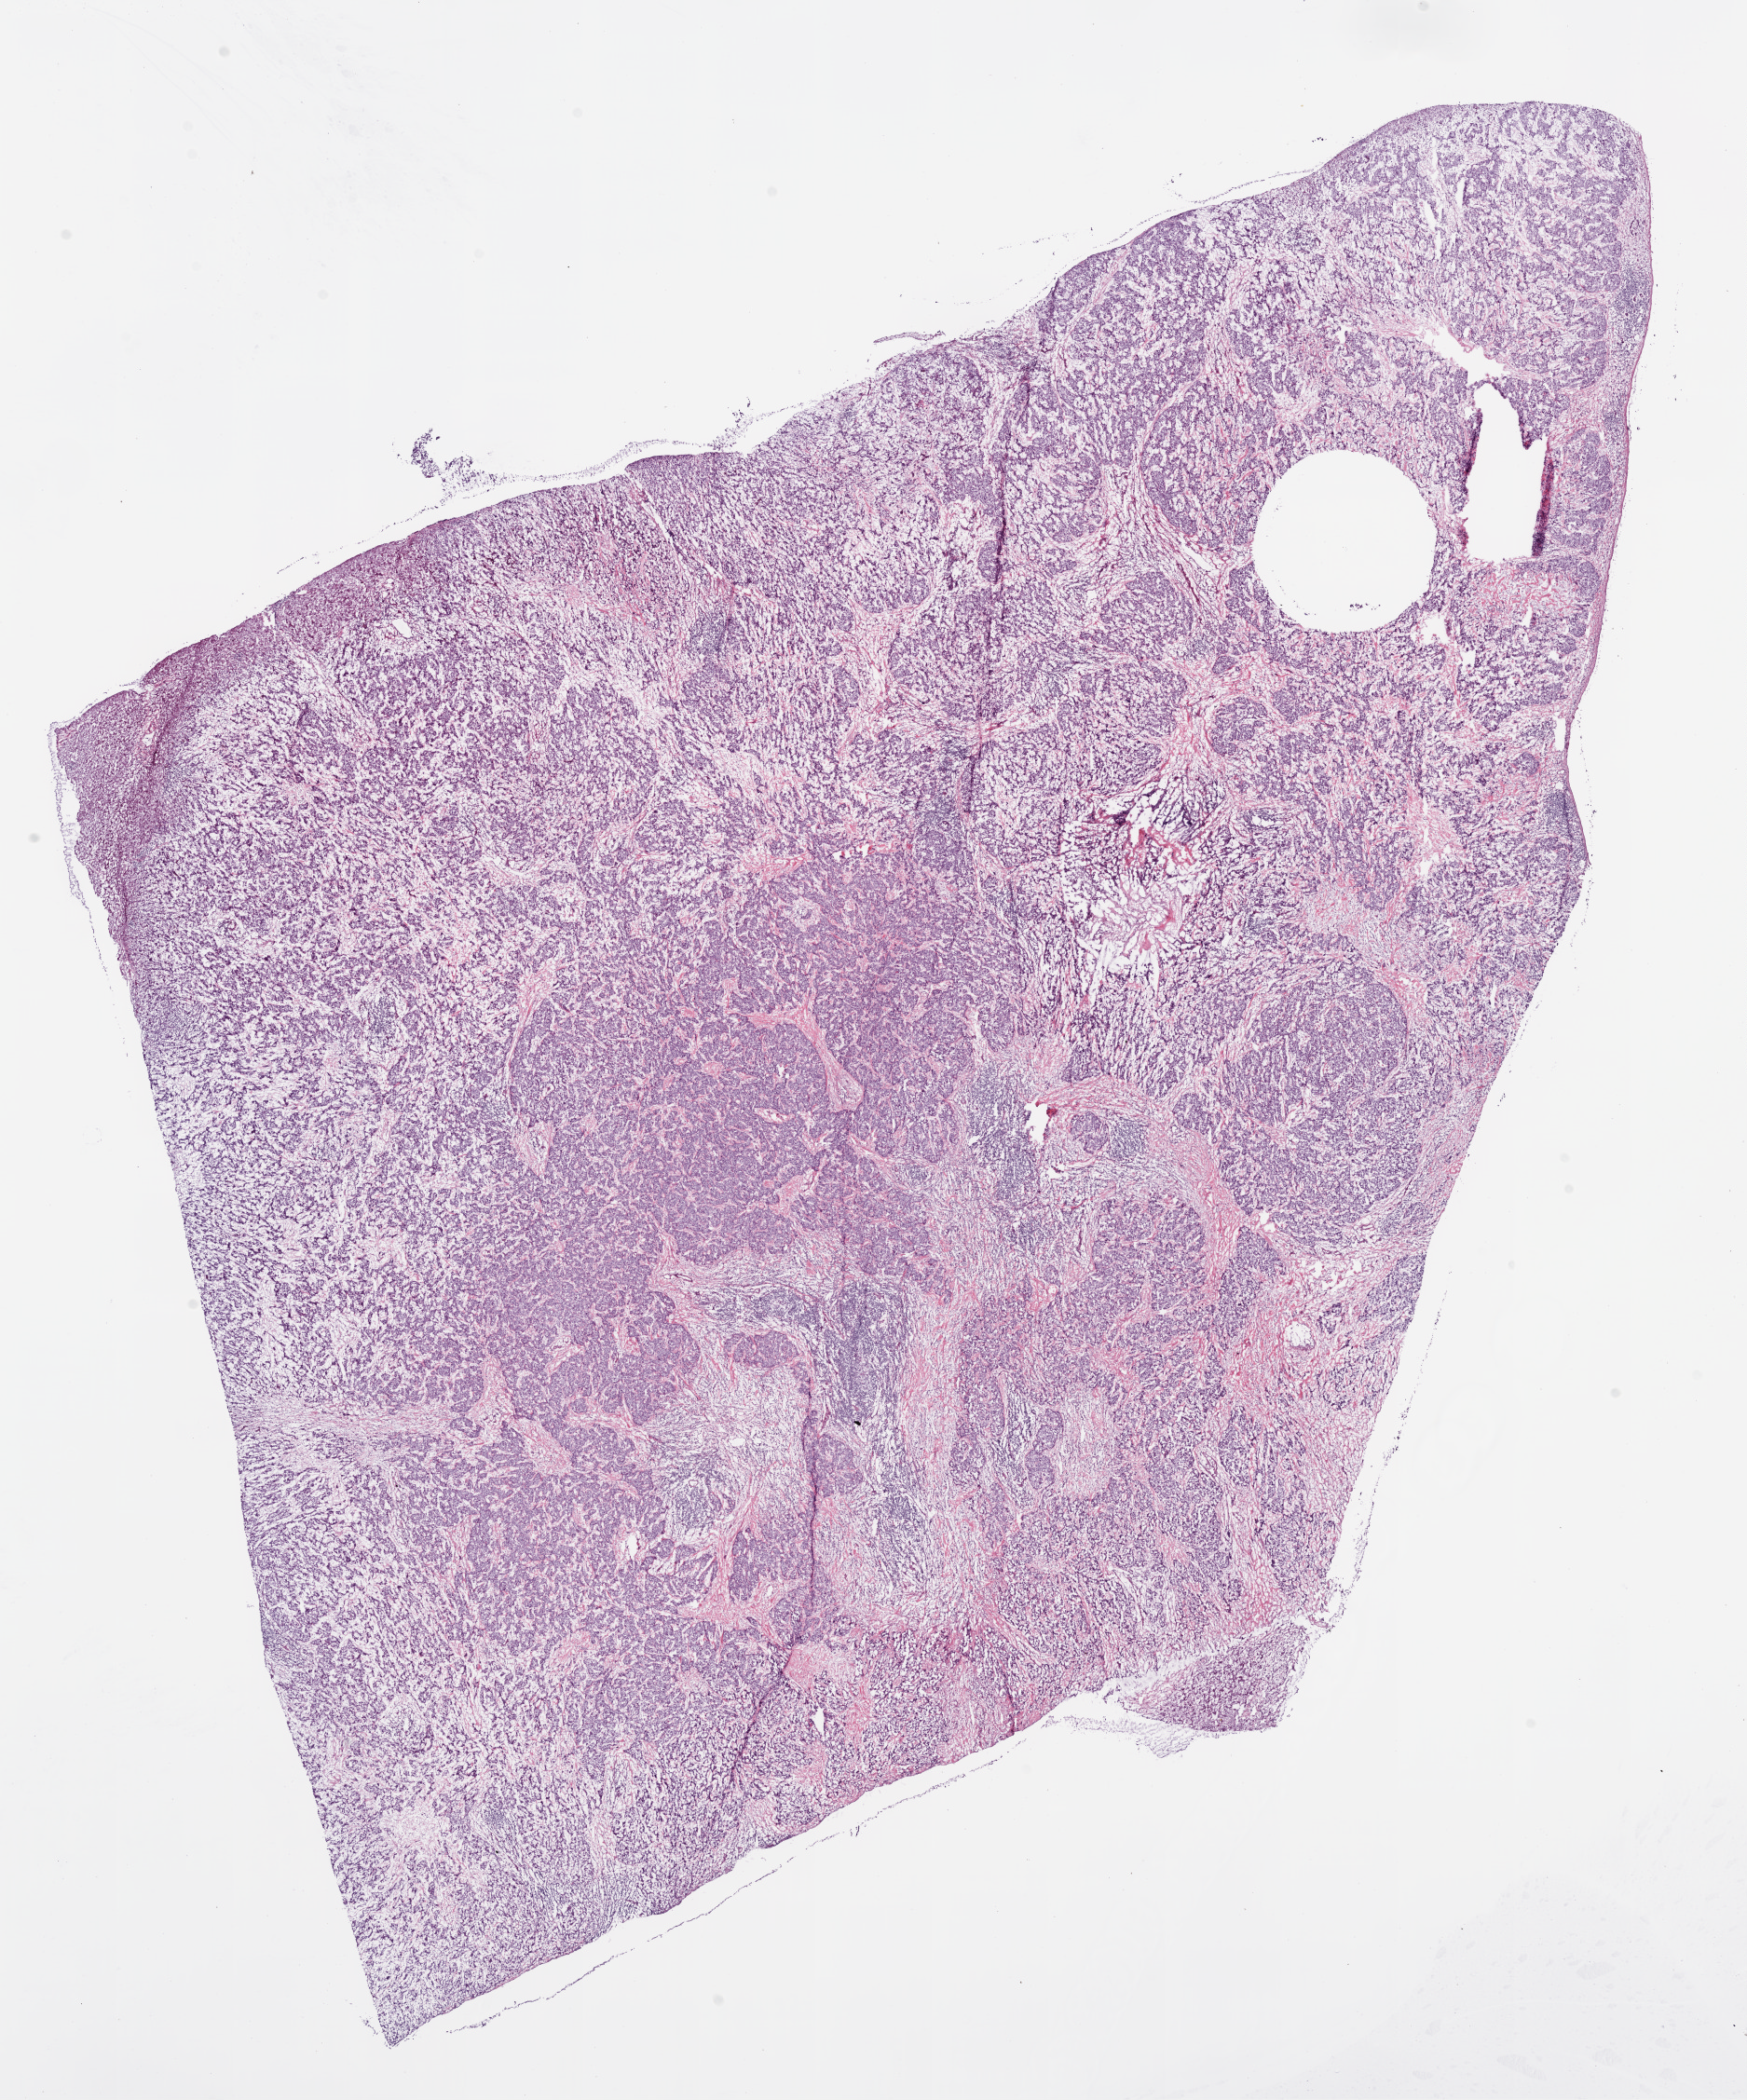
Whole-slide histology image, H&E — a low-resolution overview of the entire scanned area, about 15.0 x 18.1 mm (acquisition: 20x scan). Frozen section from the bottom of the tissue portion. Liver, primary tumour sample. Male patient; age at initial diagnosis 44 years. Histologic grade: G2 (moderately differentiated). Pathologist review of this section (percent, as recorded): tumour cells 77%, tumour nuclei 85%, normal cells 0%, stromal cells 20%, necrosis 3%.
Pathologic diagnosis: Hepatocellular carcinoma, NOS. AJCC pathologic stage: II.